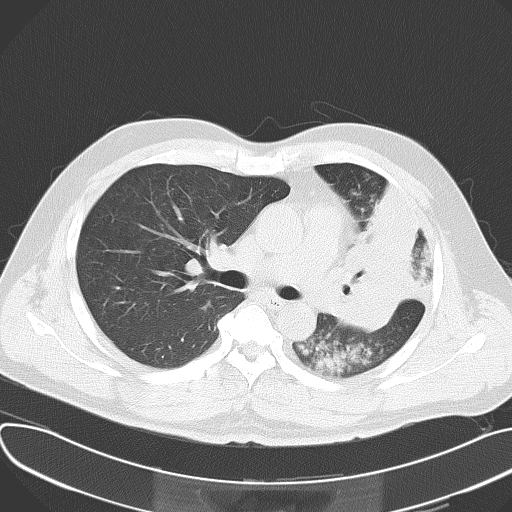
Chest CT, one axial slice. Position 39 of 62 along the scan axis. Reconstruction kernel B70f. 120 kVp. Lung window (W 1500 / L -600 HU). 5 mm slice thickness. 512 × 512 image matrix, field of view 377 × 377 mm. Patient: male, 48 years. From the clinical record (not read from this slice): clinical TNM (as recorded): T4 N0 M0.
Structures marked on this image (rectangle marked by the reading radiologist):
- lung tumour (recorded histology: adenocarcinoma): bounding box (x1, y1, x2, y2) in pixels: (341, 180, 426, 339)